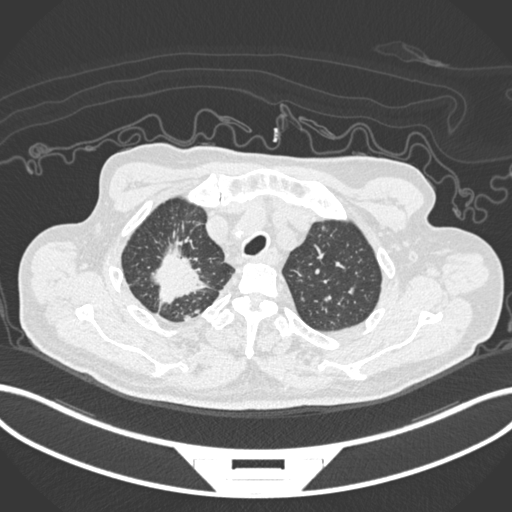
Chest CT, one axial slice. Position 184 of 207 along the scan axis. 120 kVp. Lung window (W 1500 / L -600 HU). 512 × 512 image matrix, field of view 400 × 400 mm. Patient: male, 69 years. From the clinical record (not read from this slice): clinical TNM (as recorded): T1c N1 M1.
Outlined on this slice (rectangle marked by the reading radiologist):
- lung tumour (recorded histology: adenocarcinoma): box from (x=148, y=235) to (x=213, y=307) px